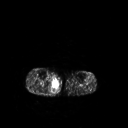
FDG PET of an extremity soft-tissue mass (from a PET/CT study), one axial slice; slice 145 of 267 in the series (ordered by position); 3.27 mm slice thickness; 128 × 128 image matrix, field of view 500 × 500 mm. Male patient, age 69 years. From the clinical record (not read from this slice): histological type: pleiomorphic liposarcoma; grade: high; site of the primary tumour: right calf.
Annotated regions visible in this slice (expert contour drawn on MRI and transferred to this co-registered scan by the dataset authors):
- gross tumour volume including surrounding oedema: bounding box <50,77,59,89> (left, top, right, bottom; pixels)
- gross tumour volume (mass): <53,80,57,85>